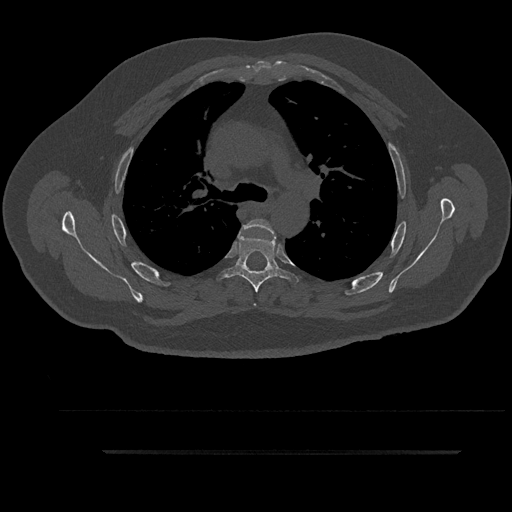
CT including the spine, one axial slice; position 635 of 797 along the scan axis; reconstruction kernel Br40s/3; bone window (W 1800 / L 400 HU); 0.5 mm slice thickness; 512 × 512 image matrix. Patient: male, 63 years. From the clinical record (not read from this slice): primary cancer: renal; vertebrae with lytic lesions (as recorded): T8.
Structures marked on this image (semi-automatic segmentation, software-assisted and operator-edited):
- T4 vertebra: bounding box (x1, y1, x2, y2) in pixels: (238, 219, 274, 305)
- T5 vertebra: (217, 229, 299, 293)